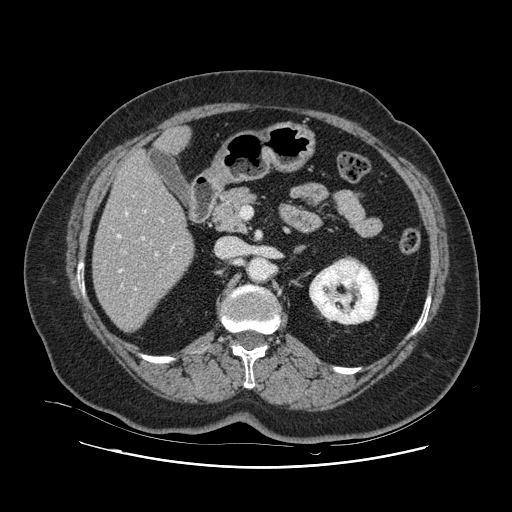
Contrast-enhanced abdominal CT, one axial slice; position 47 of 132 along the scan axis; 120 kVp; intravenous contrast given; soft-tissue window (W 400 / L 40 HU); 2.5 mm slice thickness; 512 × 512 image matrix, field of view 391 × 391 mm. Female patient, age 73 years. From the clinical record (not read from this slice): diagnosis: colorectal cancer liver metastases, imaged before liver resection; multiple liver metastases: no; largest metastasis: 7 cm.
Outlined on this slice (expert manual segmentation):
- hepatic veins: box from (x=117, y=211) to (x=174, y=287) px
- liver: (x=94, y=129)–(x=194, y=331)
- planned liver remnant (the part of the liver to remain after resection): (x=94, y=155)–(x=194, y=332)
- portal vein (with intrahepatic branches): (x=134, y=220)–(x=164, y=290)